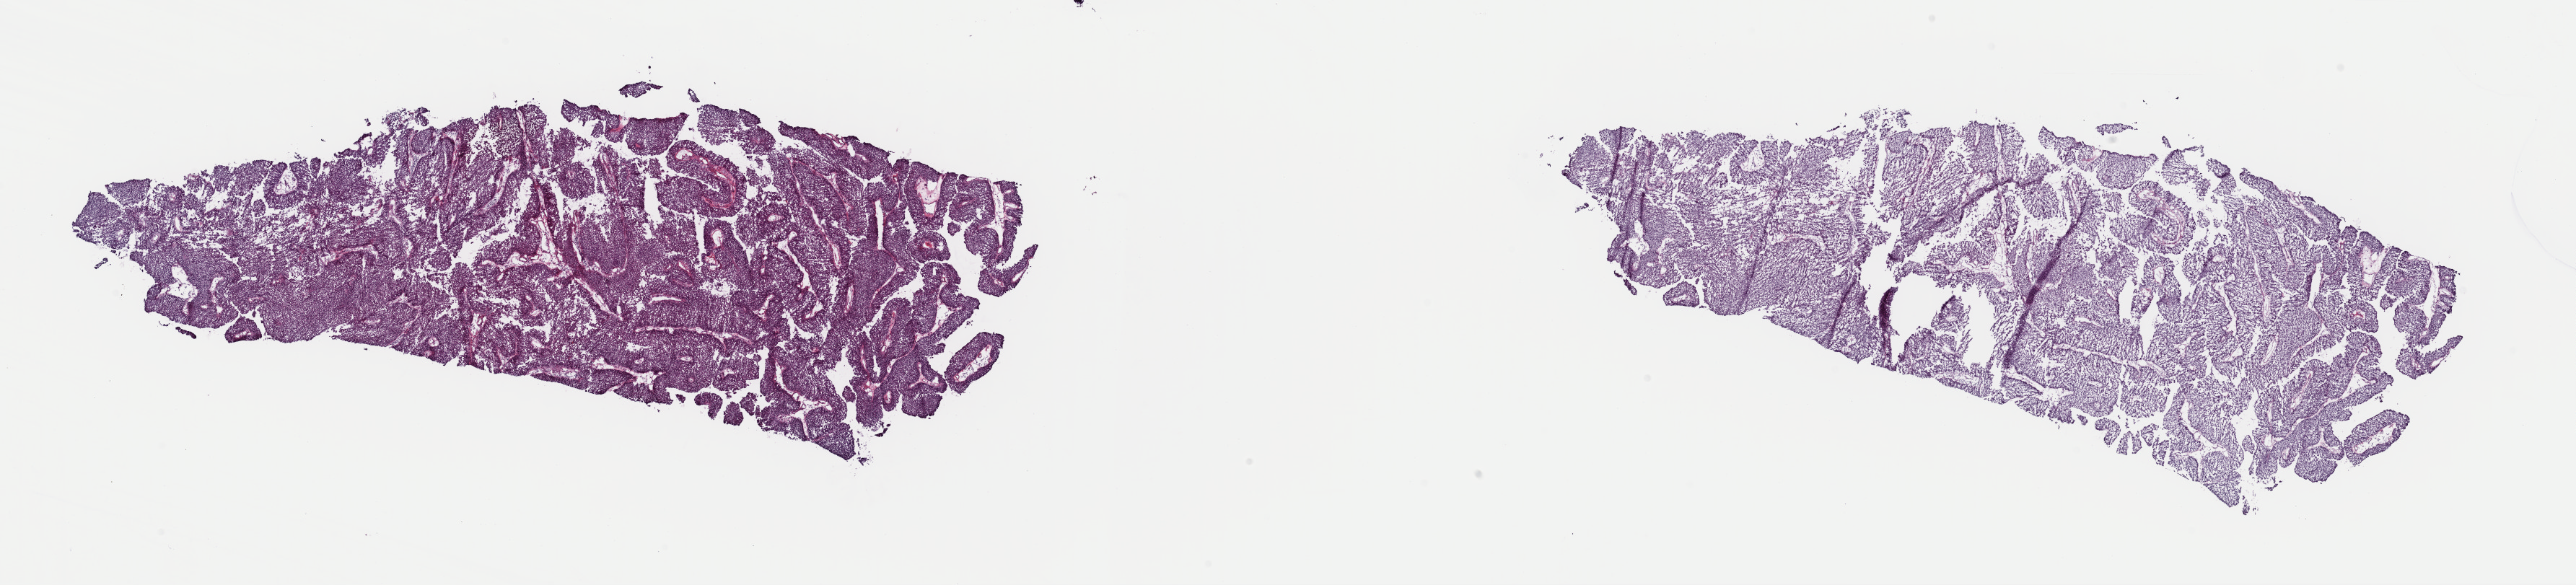
Whole-slide histology image, Hematoxylin and eosin (H&E) stained, low-resolution overview of the scanned area, about 28.2 x 6.4 mm (acquisition: 40x scan). Frozen section from the top of the tissue portion. Primary tumour sample from the bladder. Patient: male, age at initial diagnosis 67 years. Histologic grade: low grade. Composition of this section per pathologist review: tumour cells 100%, tumour nuclei 80%, normal cells 0%, stromal cells 0%, necrosis 0%. Infiltration values recorded for this section: lymphocyte infiltration 1%, monocyte infiltration 0%, neutrophil infiltration 0%.
* TNM: T2a N0 M0
* AJCC pathologic stage: II (7th edition)
* diagnosis: Transitional cell carcinoma